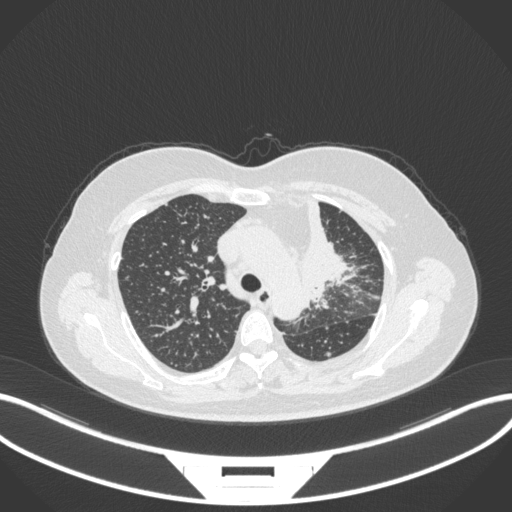
Chest CT, one axial slice; slice 240 of 348 in the series (ordered by position); reconstruction kernel B31f; 120 kVp; lung window (W 1500 / L -600 HU); 1 mm slice thickness; 512 × 512 image matrix. Female patient, age 49 years. From the clinical record (not read from this slice): clinical TNM (as recorded): T1c N0 M1.
Annotated regions visible in this slice (bounding box drawn by a radiologist):
- lung tumour (recorded histology: adenocarcinoma): bounding box <298,195,349,304> (left, top, right, bottom; pixels)